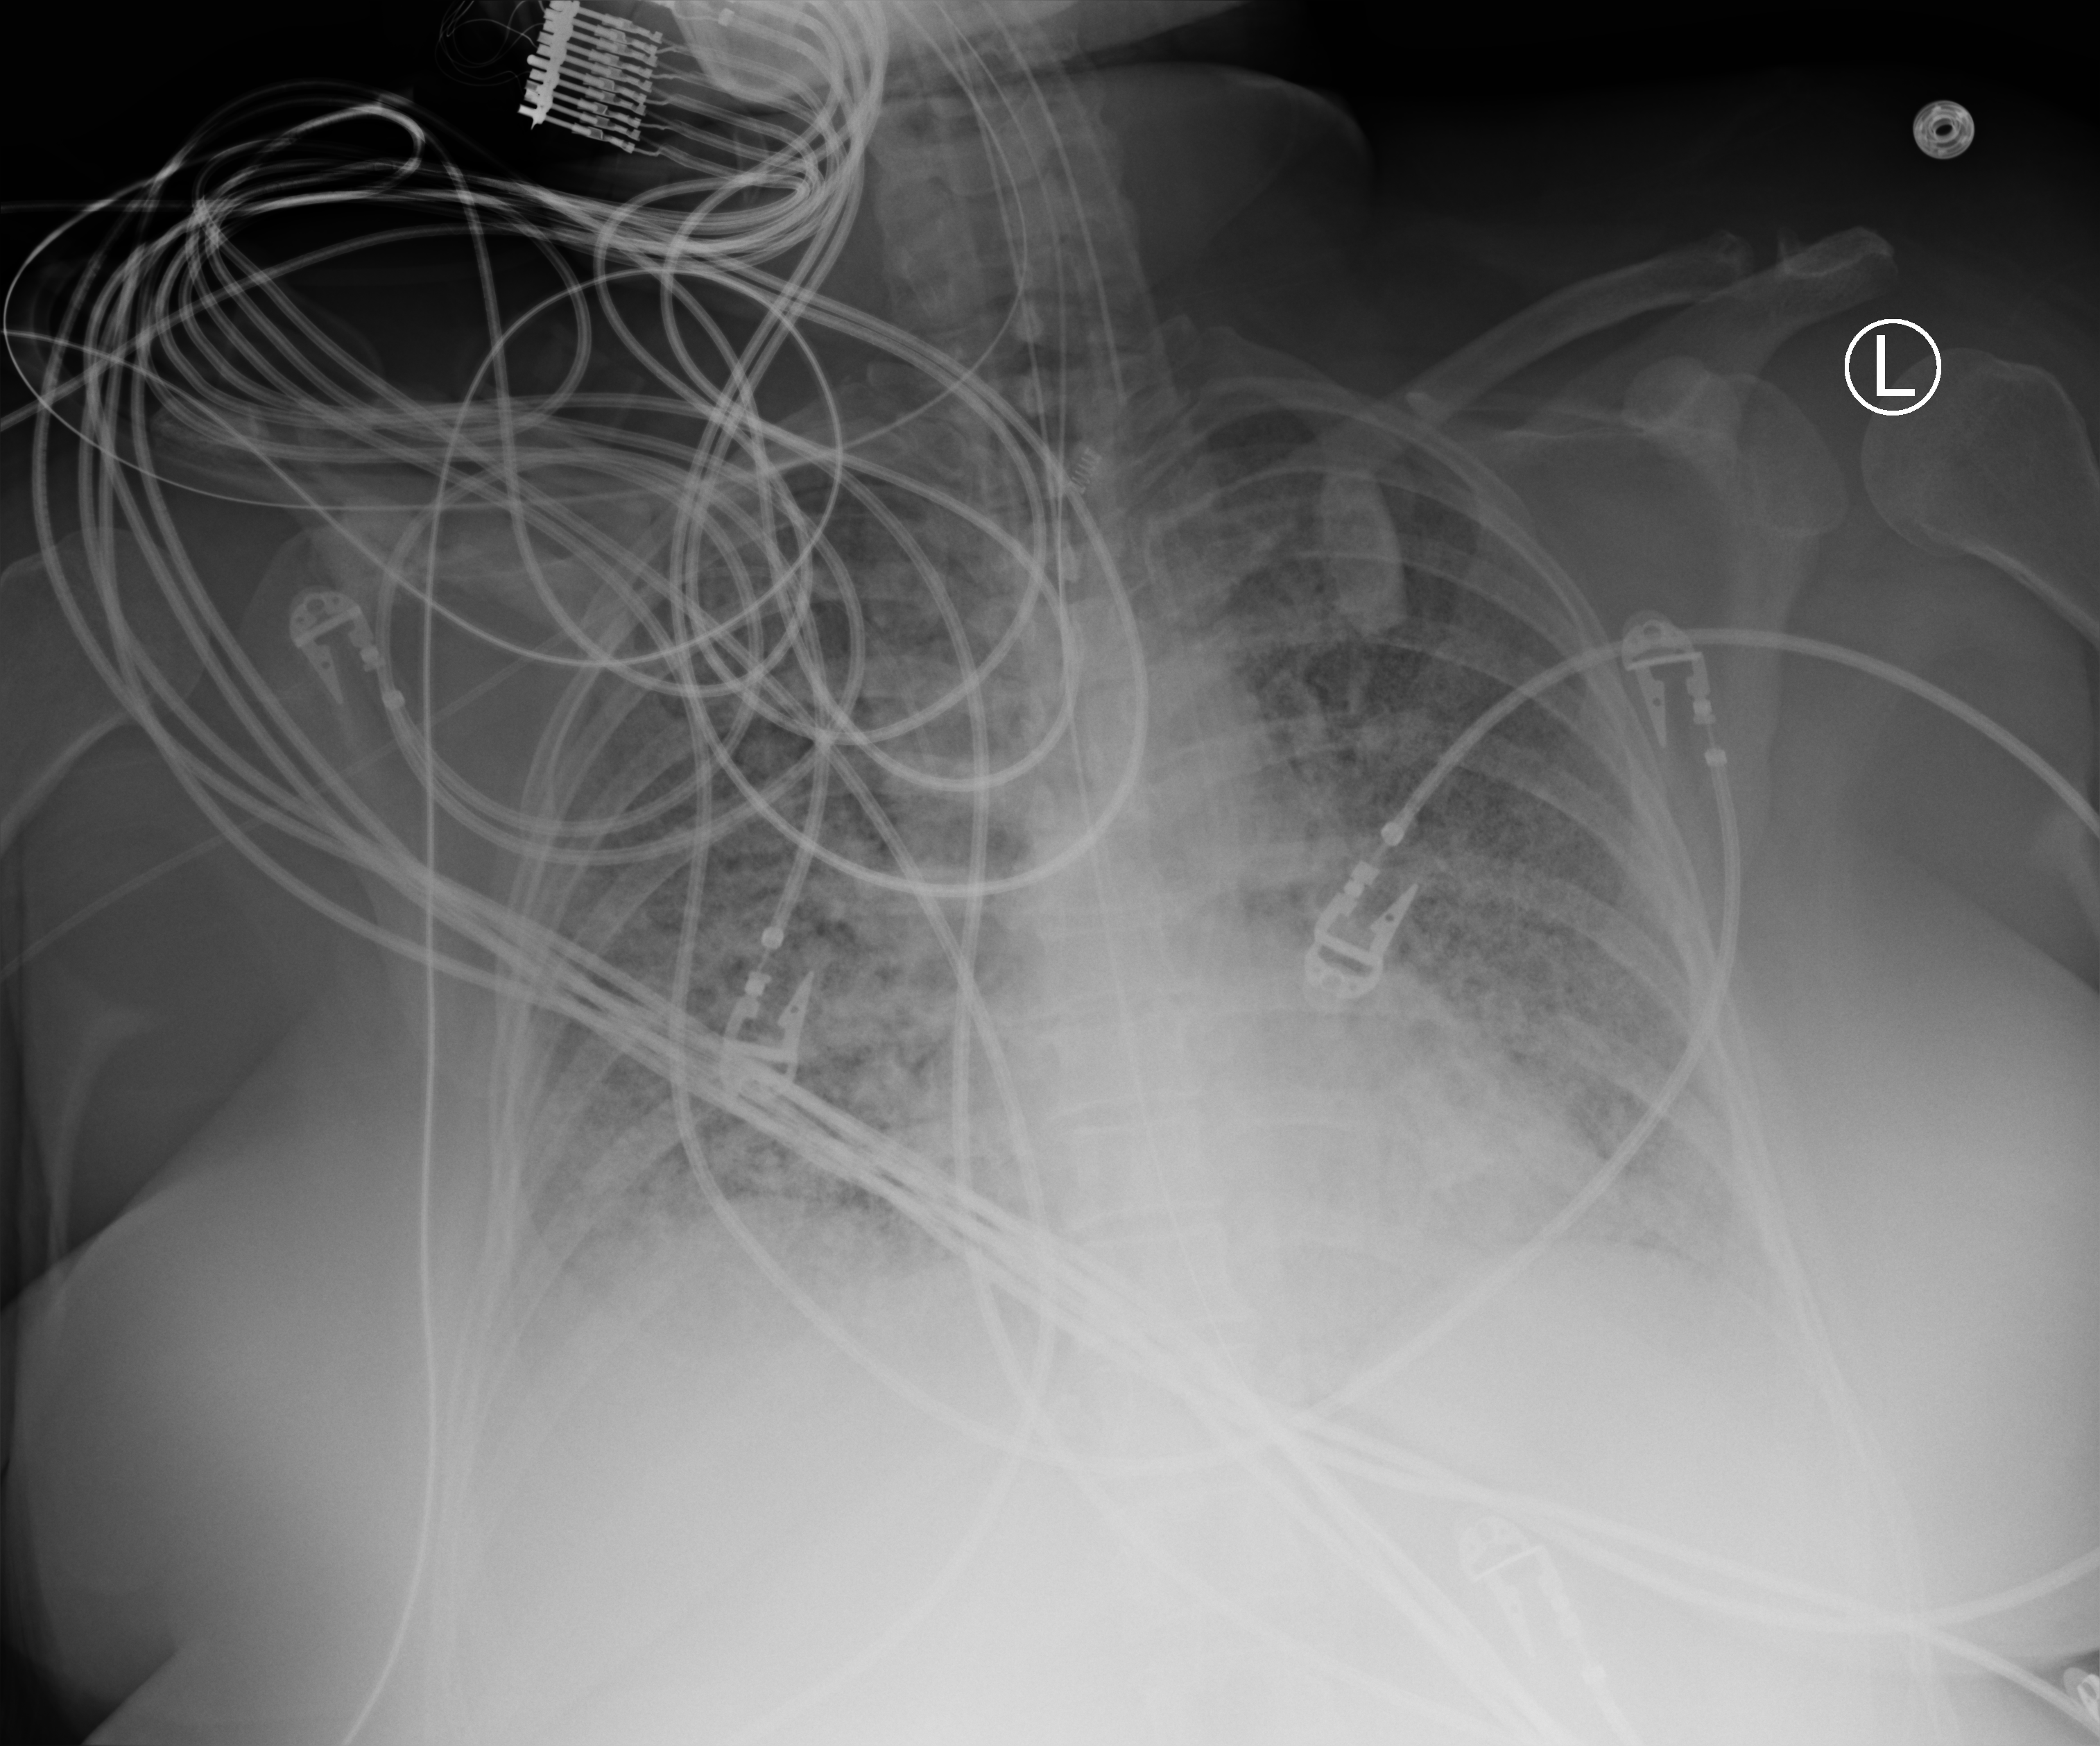
Portable chest radiograph, anteroposterior (AP) projection. Female patient hospitalised with COVID-19, age 18–59 years.
From the hospital-stay record, not from the radiograph (when in the stay this image was taken is not recorded):
- admitted to intensive care during this hospital stay: yes